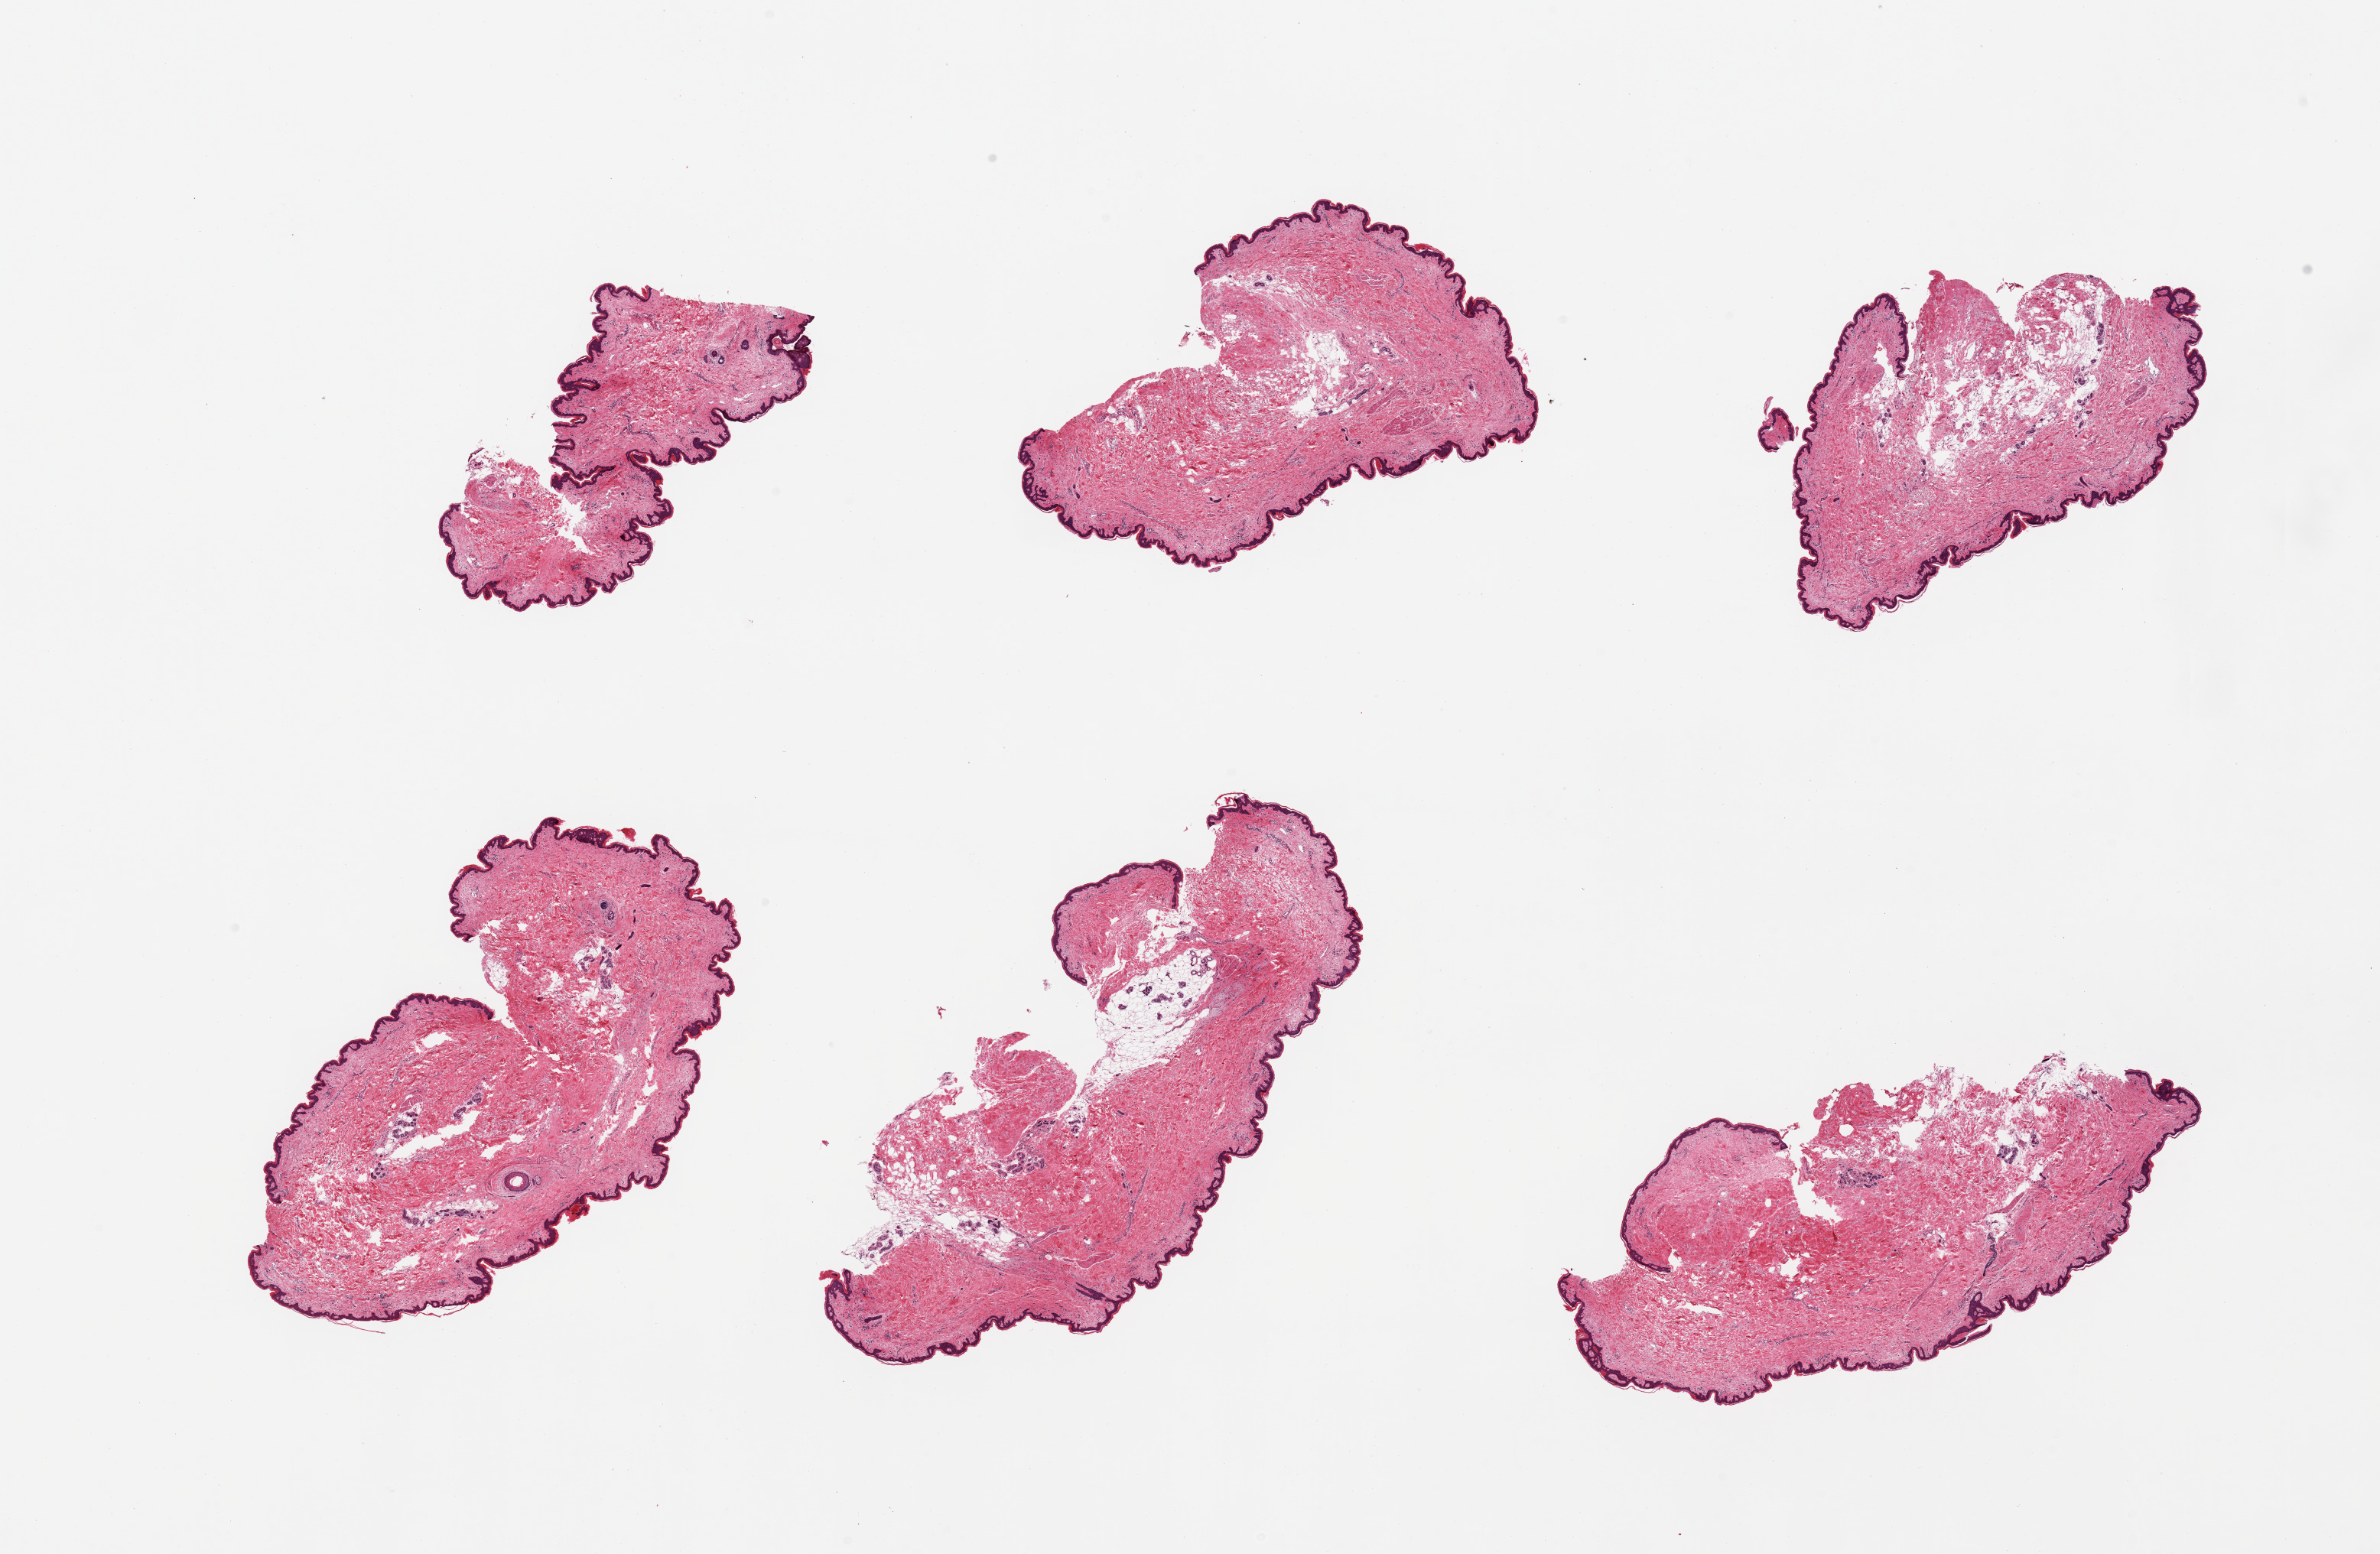
Digitized haematoxylin and eosin-stained section — whole scanned area (about 24.6 x 16.1 mm) shown as a low-resolution overview; PAXgene-fixed paraffin-embedded (PFPE) section; target tissue: skin of suprapubic region; donor tissue sample. Female donor.
Pathologist's review note for this sample: 6 pieces; well trimmed; 10% dermal fat.